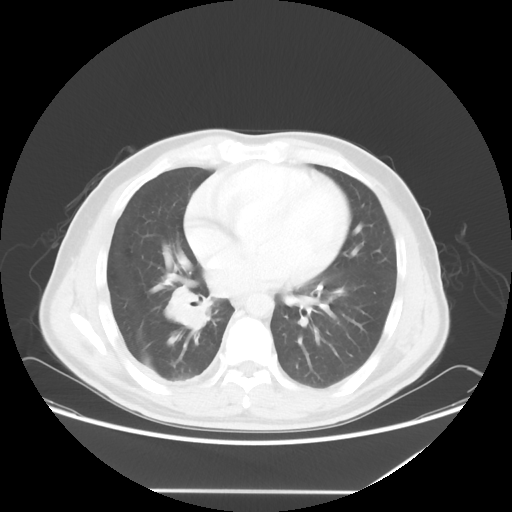
Chest CT, one axial slice. Reconstruction kernel STANDARD. 120 kVp. Lung window (W 1500 / L -600 HU). 512 × 512 image matrix, field of view 419 × 419 mm. Patient: male, 48 years. From the clinical record (not read from this slice): clinical TNM (as recorded): T3 N3 M1a.
Outlined on this slice (bounding box drawn by a radiologist):
- lung tumour (recorded histology: squamous cell carcinoma): box from (x=159, y=282) to (x=217, y=334) px